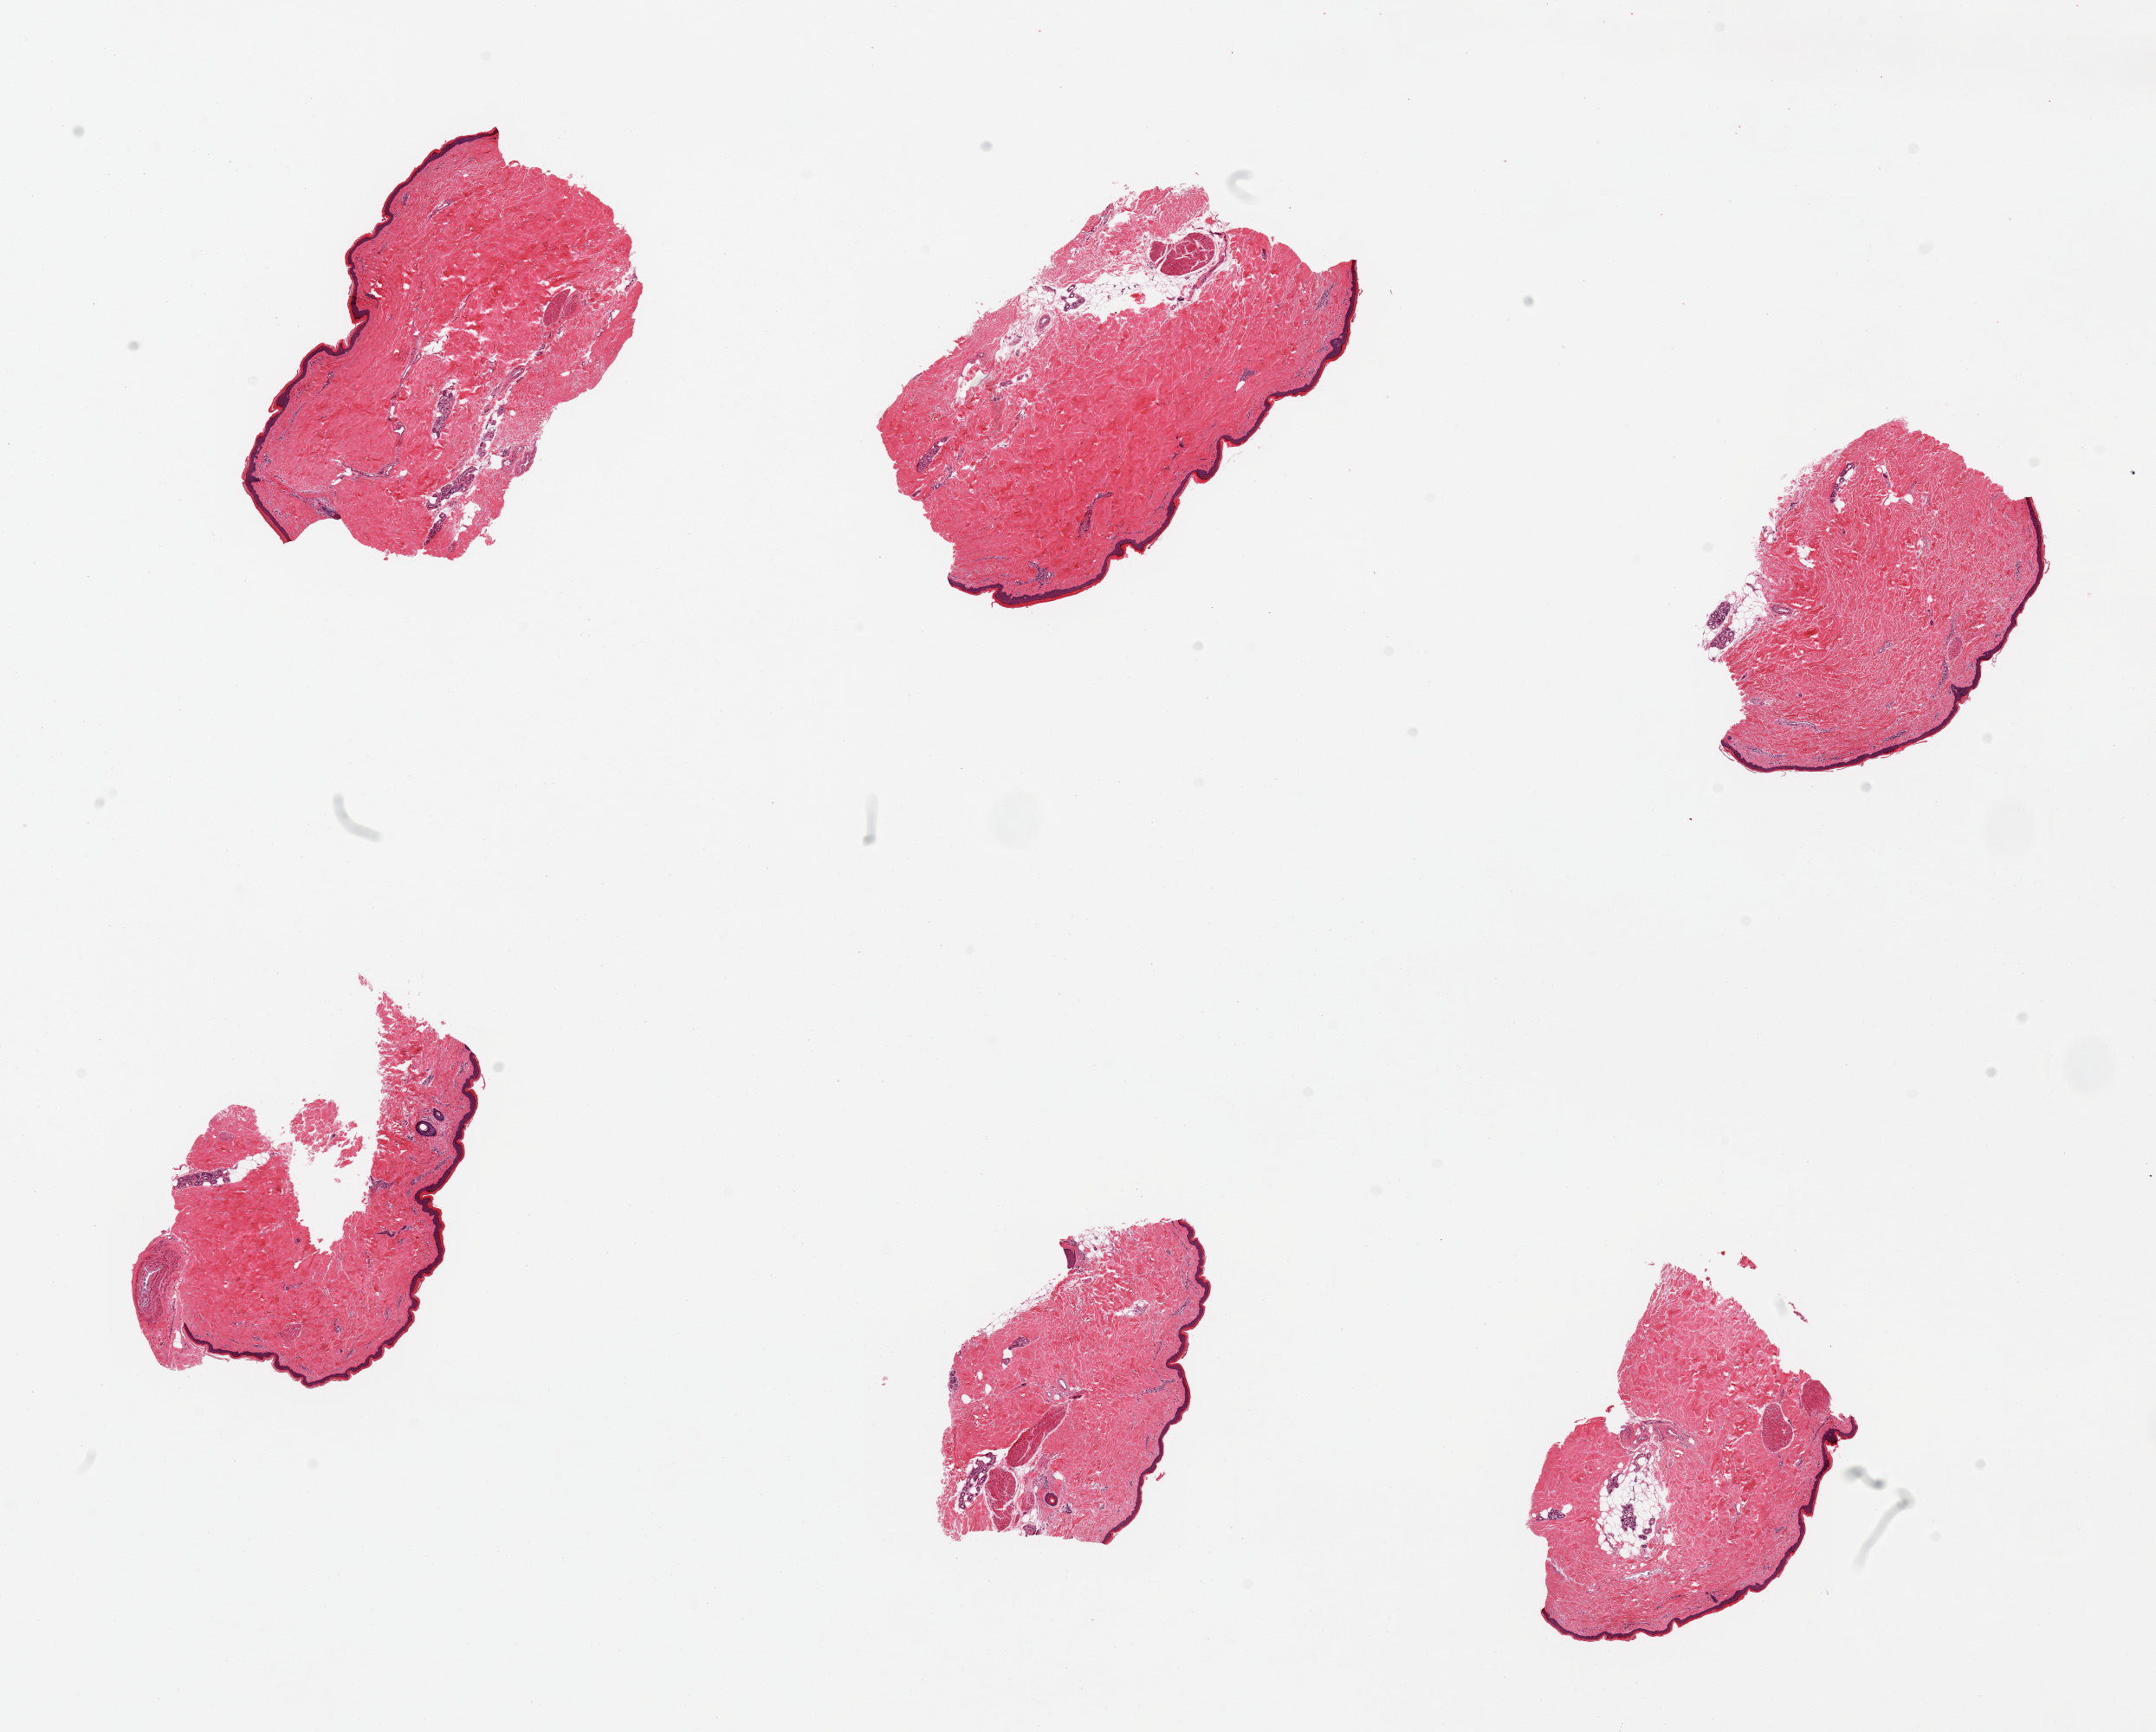
Digitized H&E-stained section — a low-resolution overview of the entire scanned area, about 19.7 x 15.8 mm; PAXgene-fixed, paraffin-embedded tissue; section of skin of lower leg (target tissue); tissue donor sample. Donor sex: female.
Review note (as recorded): 6 pieces; <10% dermal fat.